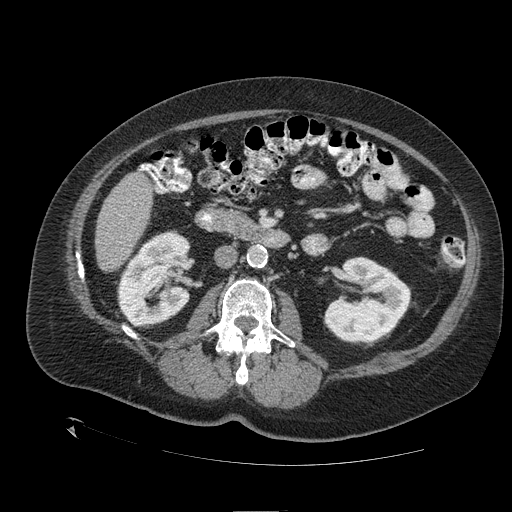
Contrast-enhanced abdominal CT (liver protocol), one axial slice; position 40 of 109 along the scan axis; one of 2 acquisitions stored at this slice position; soft-tissue window (W 400 / L 40 HU); 2.5 mm slice thickness; 512 × 512 image matrix. From the clinical record (not read from this slice): diagnosis: hepatocellular carcinoma (patient treated with transarterial chemoembolisation; whether this scan precedes or follows treatment is not stated here); TNM stage (as recorded): Stage-I; Child-Pugh class: A; tumour differentiation: no biopsy.
Outlined on this slice (semi-automatic segmentation, software-assisted and operator-edited):
- liver parenchyma outside the tumour (the mass and vessels are separate outlines, so this box may not span the whole liver): bounding box (x1, y1, x2, y2) in pixels: (94, 170, 152, 270)